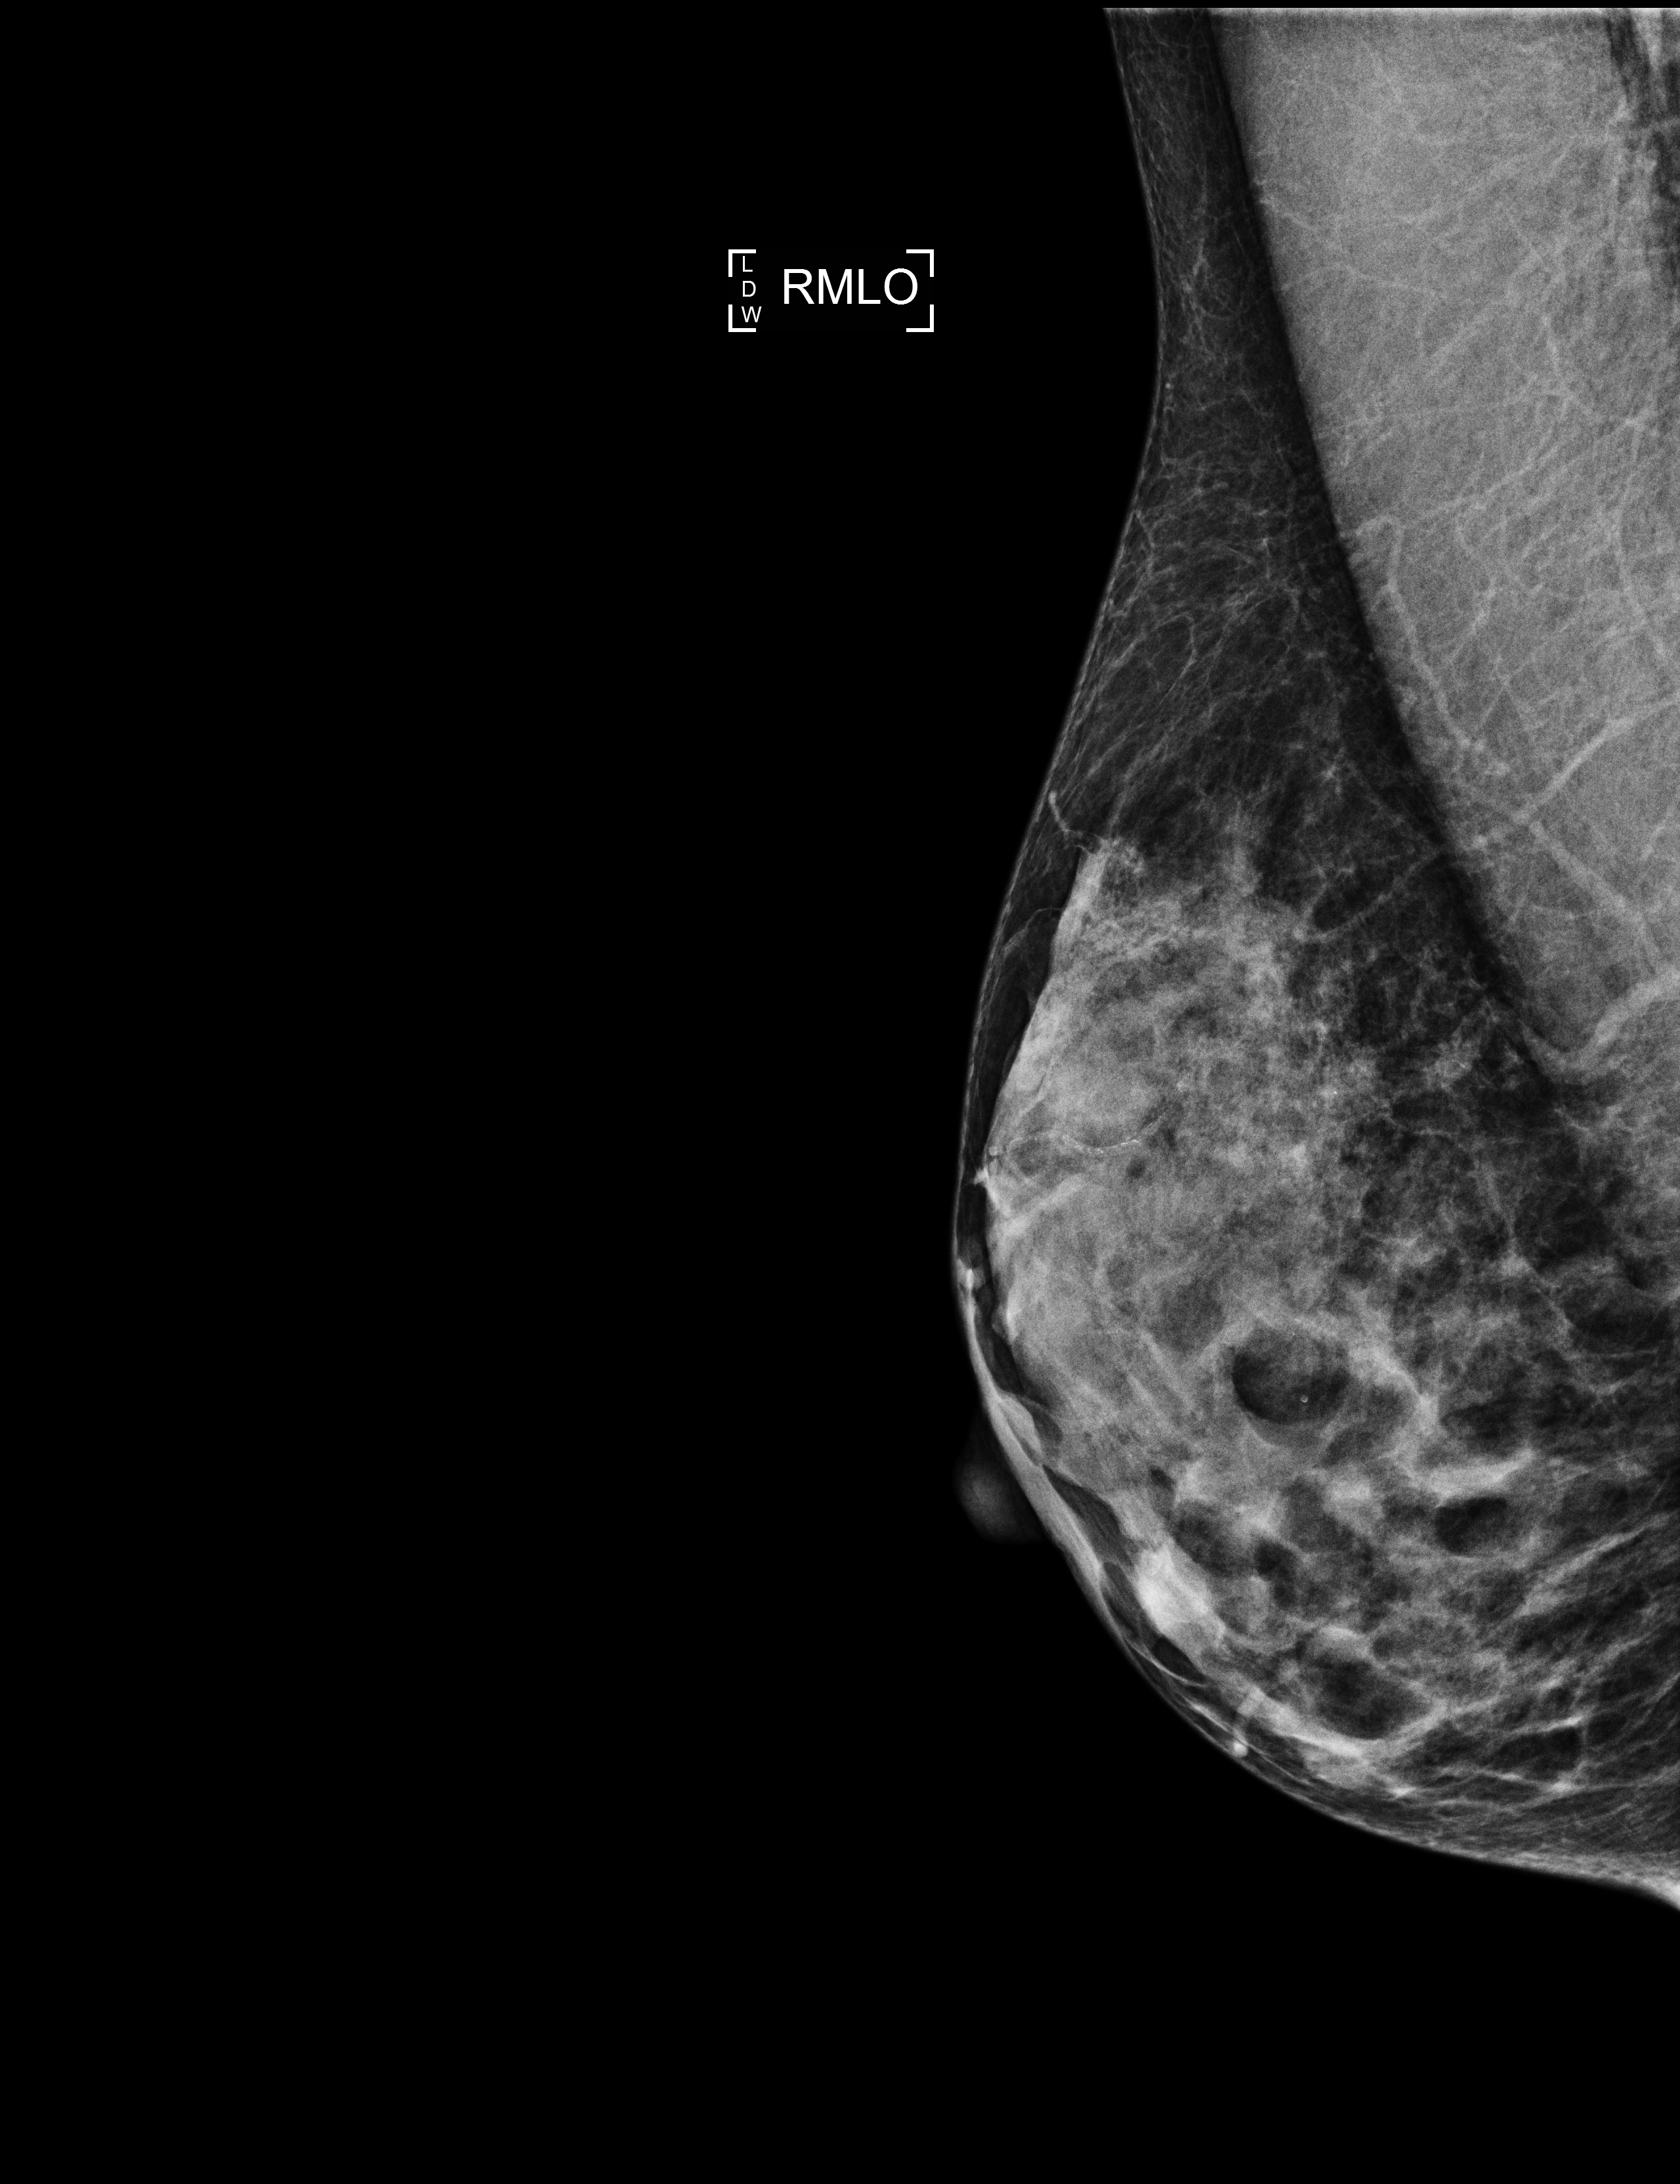
Digital mammogram (FFDM), right breast, MLO view, annual screening mammography examination, compressed breast thickness 35 mm. Patient aged 58 years (female).
Breast density at the screening exam (both breasts): heterogeneously dense (BI-RADS density category c). Final BI-RADS assessment for this screening round (tomosynthesis exam, both breasts): category 2. Recall: no recall after this screen.